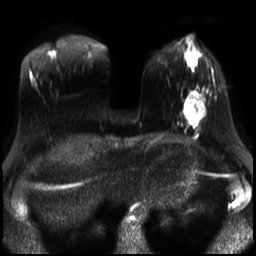
Breast MRI, one axial slice; slice 9 of 30 in the series (ordered by position); diffusion-weighted series; image 2 of 4 stored at this slice position (different b-values; order by instance number); 3 T; 256 × 256 image matrix. Female patient.
Outlined on this slice (manually delineated by an expert):
- tumour on diffusion-weighted imaging: bounding box (x1, y1, x2, y2) in pixels: (185, 105, 204, 122)